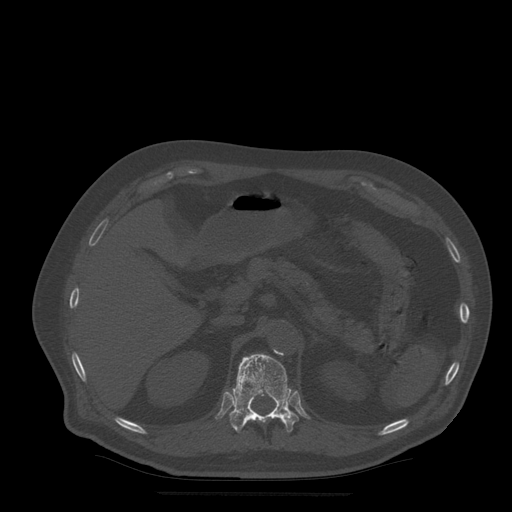
CT including the spine, one axial slice; position 223 of 522 along the scan axis; bone window (W 1800 / L 400 HU); 1.25 mm slice thickness; 512 × 512 image matrix, field of view 420 × 420 mm. Patient age 72 years. Case-level facts recorded for this patient, not image findings: primary cancer: prostate.
Structures marked on this image (semi-automatically segmented with operator editing):
- T12 vertebra: bounding box [x1, y1, x2, y2] px = [230, 354, 299, 433]